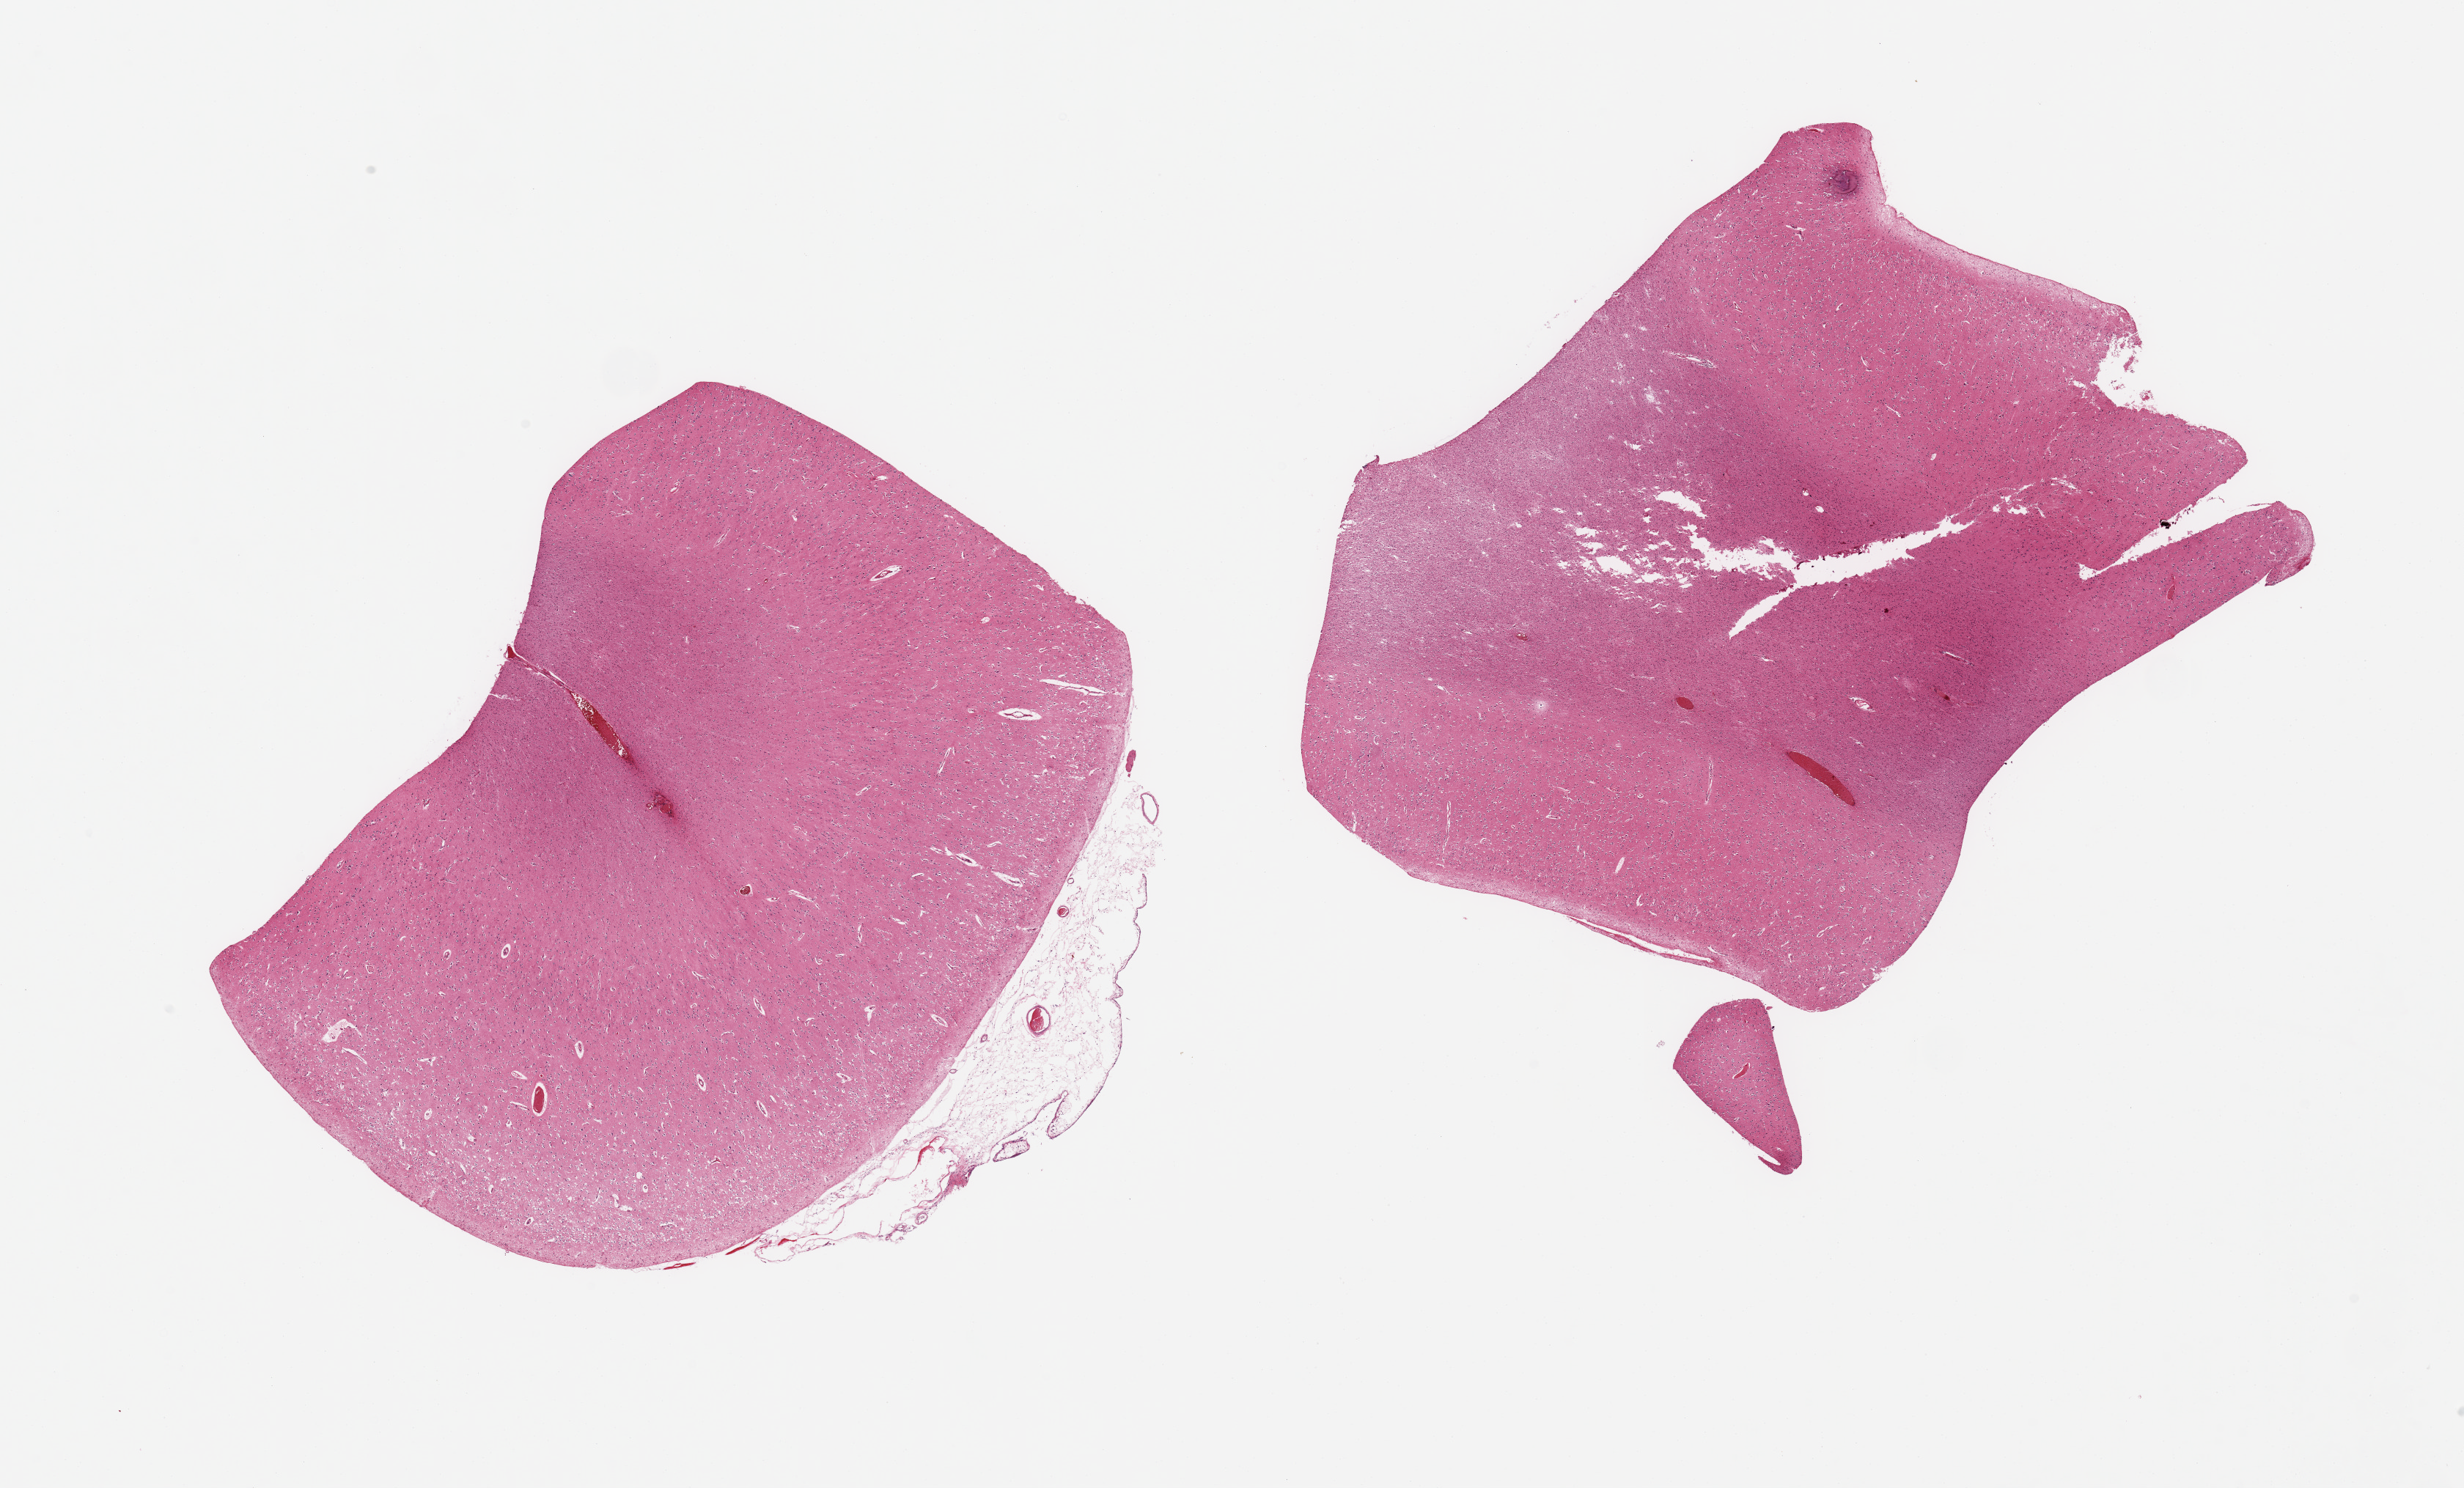
Haematoxylin and eosin whole-slide image — shown as a low-resolution overview of the whole scanned area (about 26.6 x 16.1 mm). PAXgene-fixed paraffin-embedded (PFPE) section. Section of cerebral cortex (target tissue). Donor tissue sample. Donor: male.
Pathologist's review note for this sample: 2 pieces; no abnormalities.